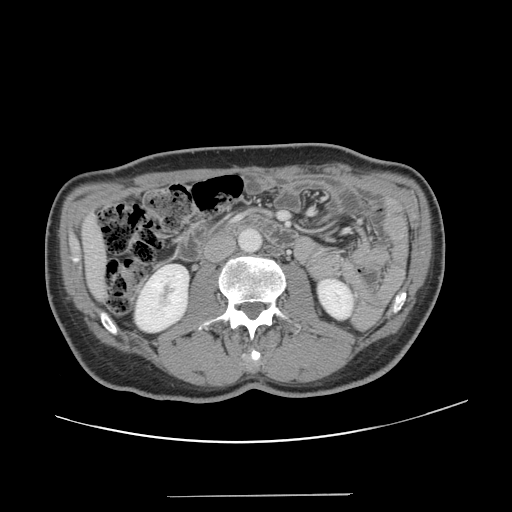
Contrast-enhanced abdominal CT, one axial slice. Intravenous contrast given. Soft-tissue window (W 400 / L 40 HU). 2.5 mm slice thickness. 512 × 512 image matrix. Male patient, age 60 years. From the clinical record (not read from this slice): diagnosis: colorectal cancer liver metastases, imaged before liver resection; multiple liver metastases: no.
Outlined on this slice (expert manual segmentation):
- liver: bounding box (x1, y1, x2, y2) in pixels: (84, 220, 104, 298)
- planned liver remnant (the part of the liver to remain after resection): (84, 220, 105, 296)